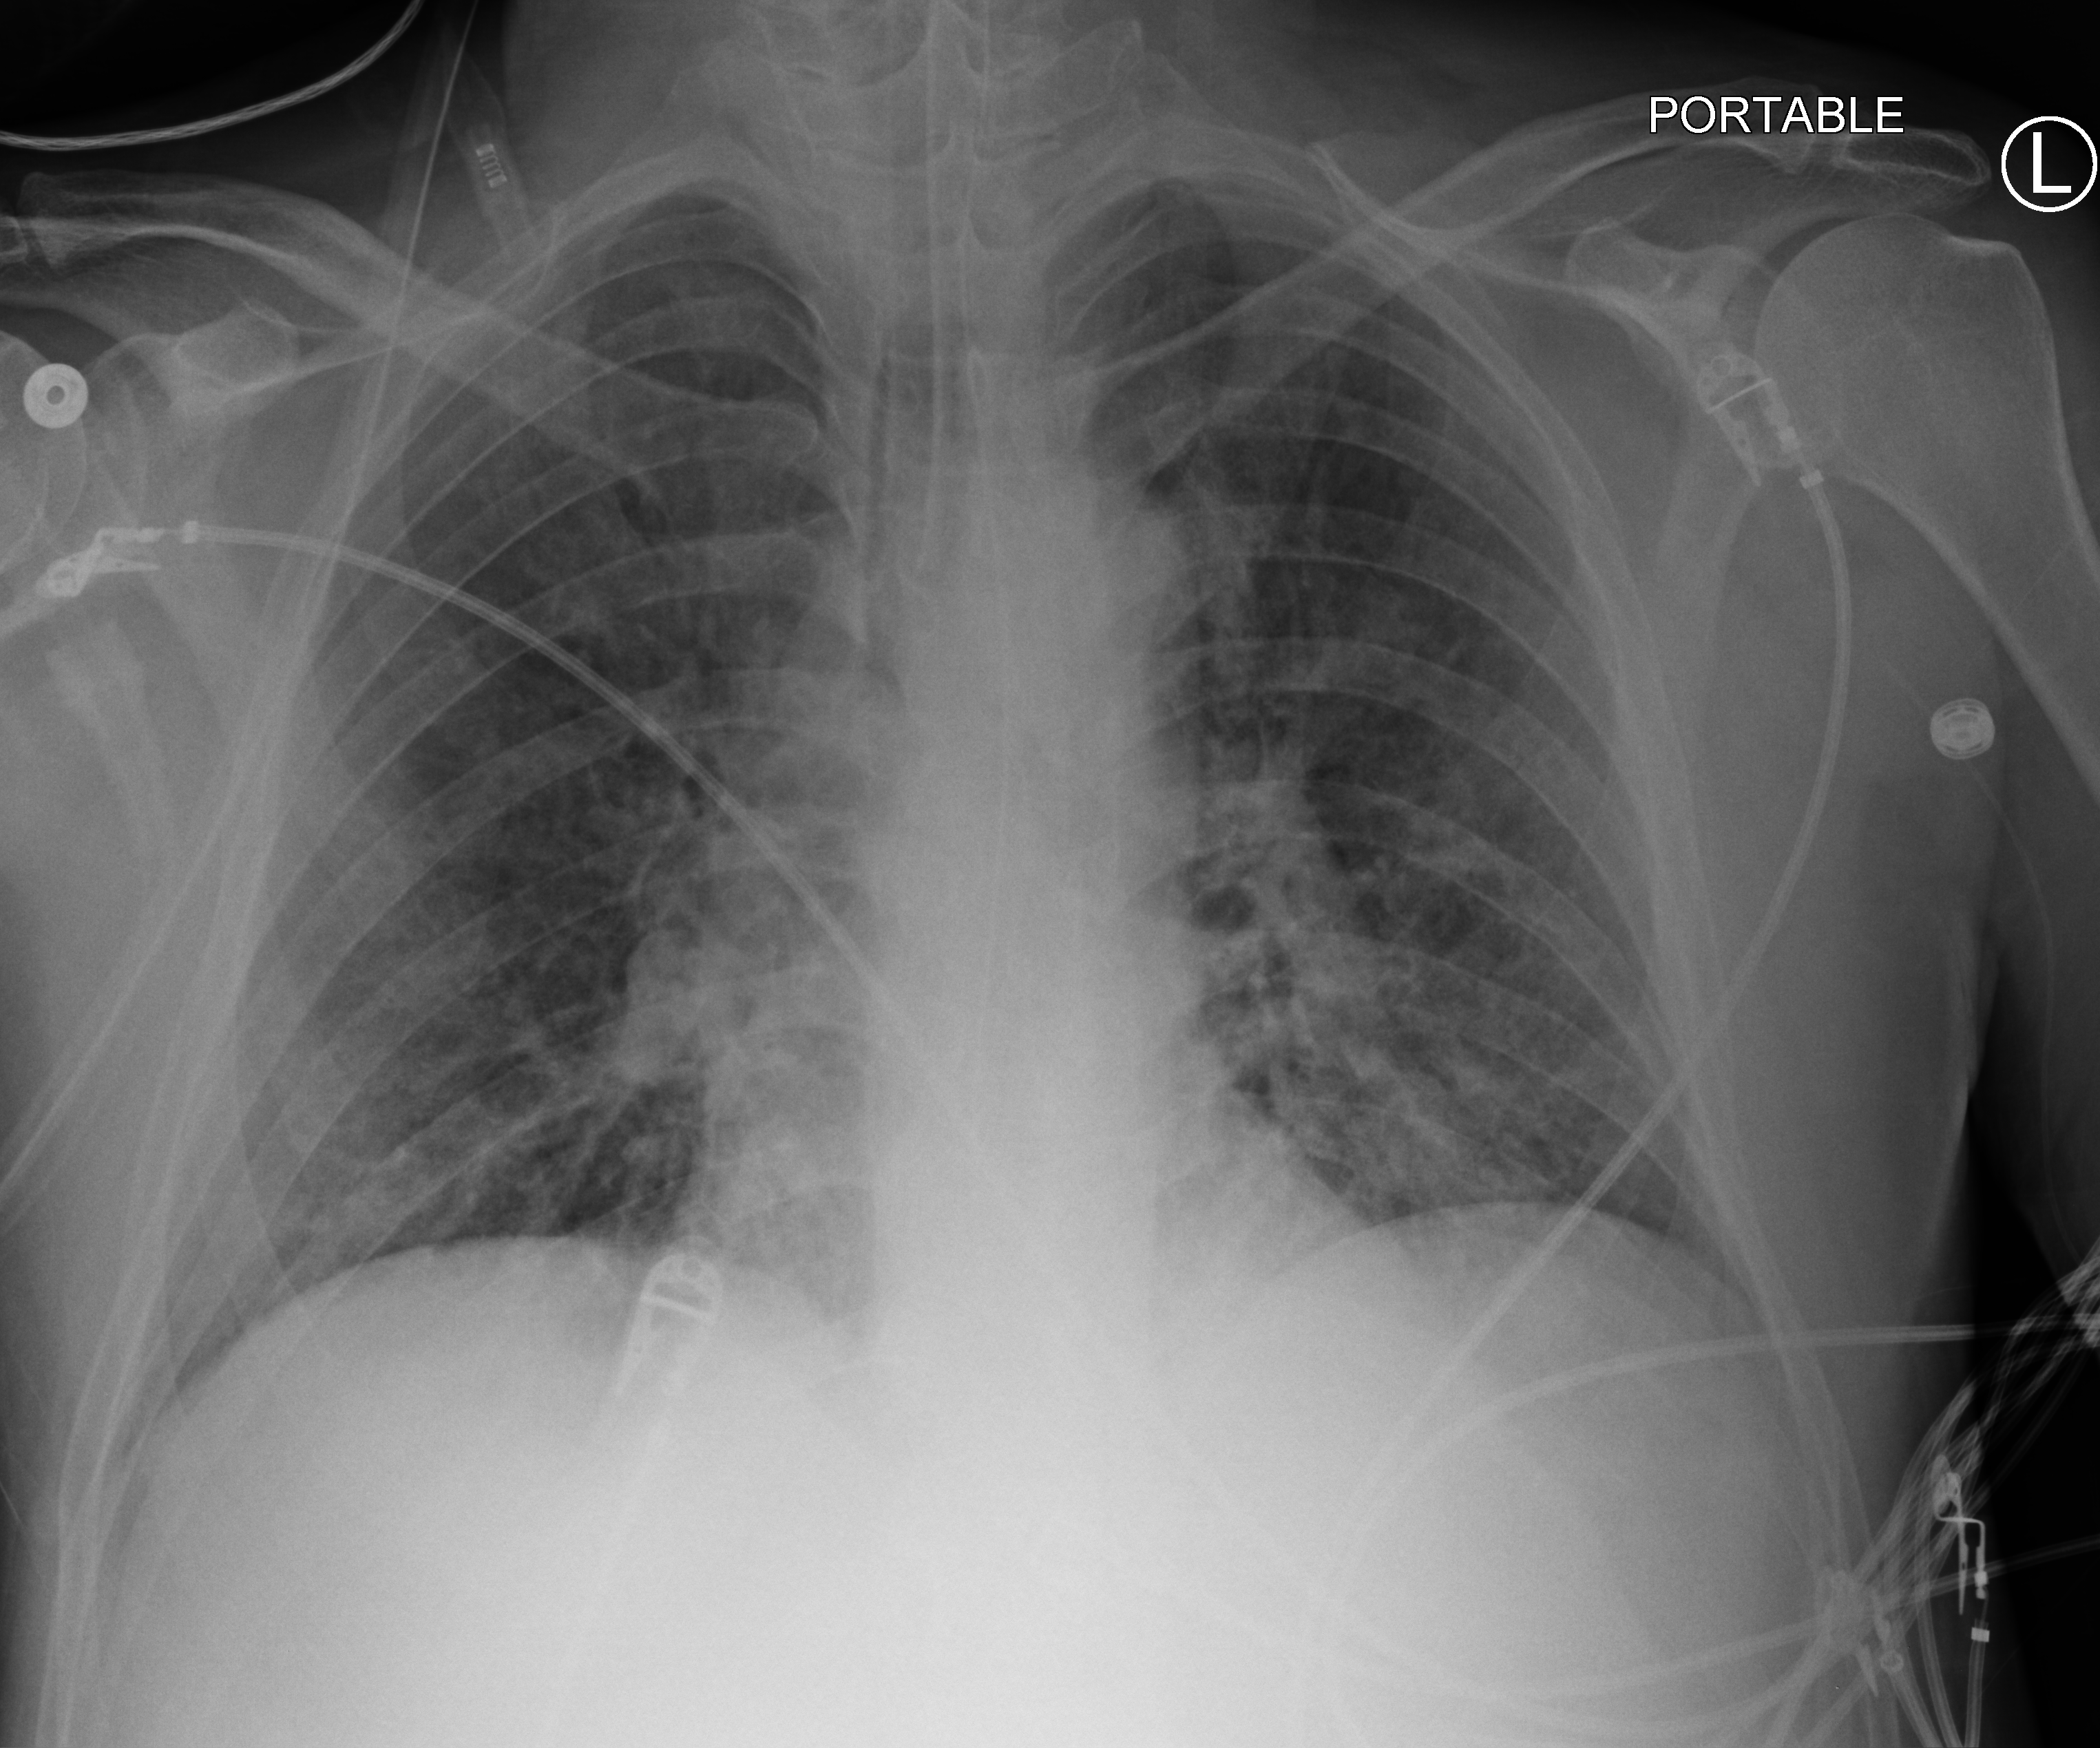
Bedside chest radiograph (computed radiography), anteroposterior (AP) projection. Patient hospitalised with COVID-19; male, aged 18–59 years.
From the hospital-stay record, not from the radiograph (when in the stay this image was taken is not recorded): admitted to intensive care during this hospital stay: no; mechanically ventilated during this hospital stay: yes.